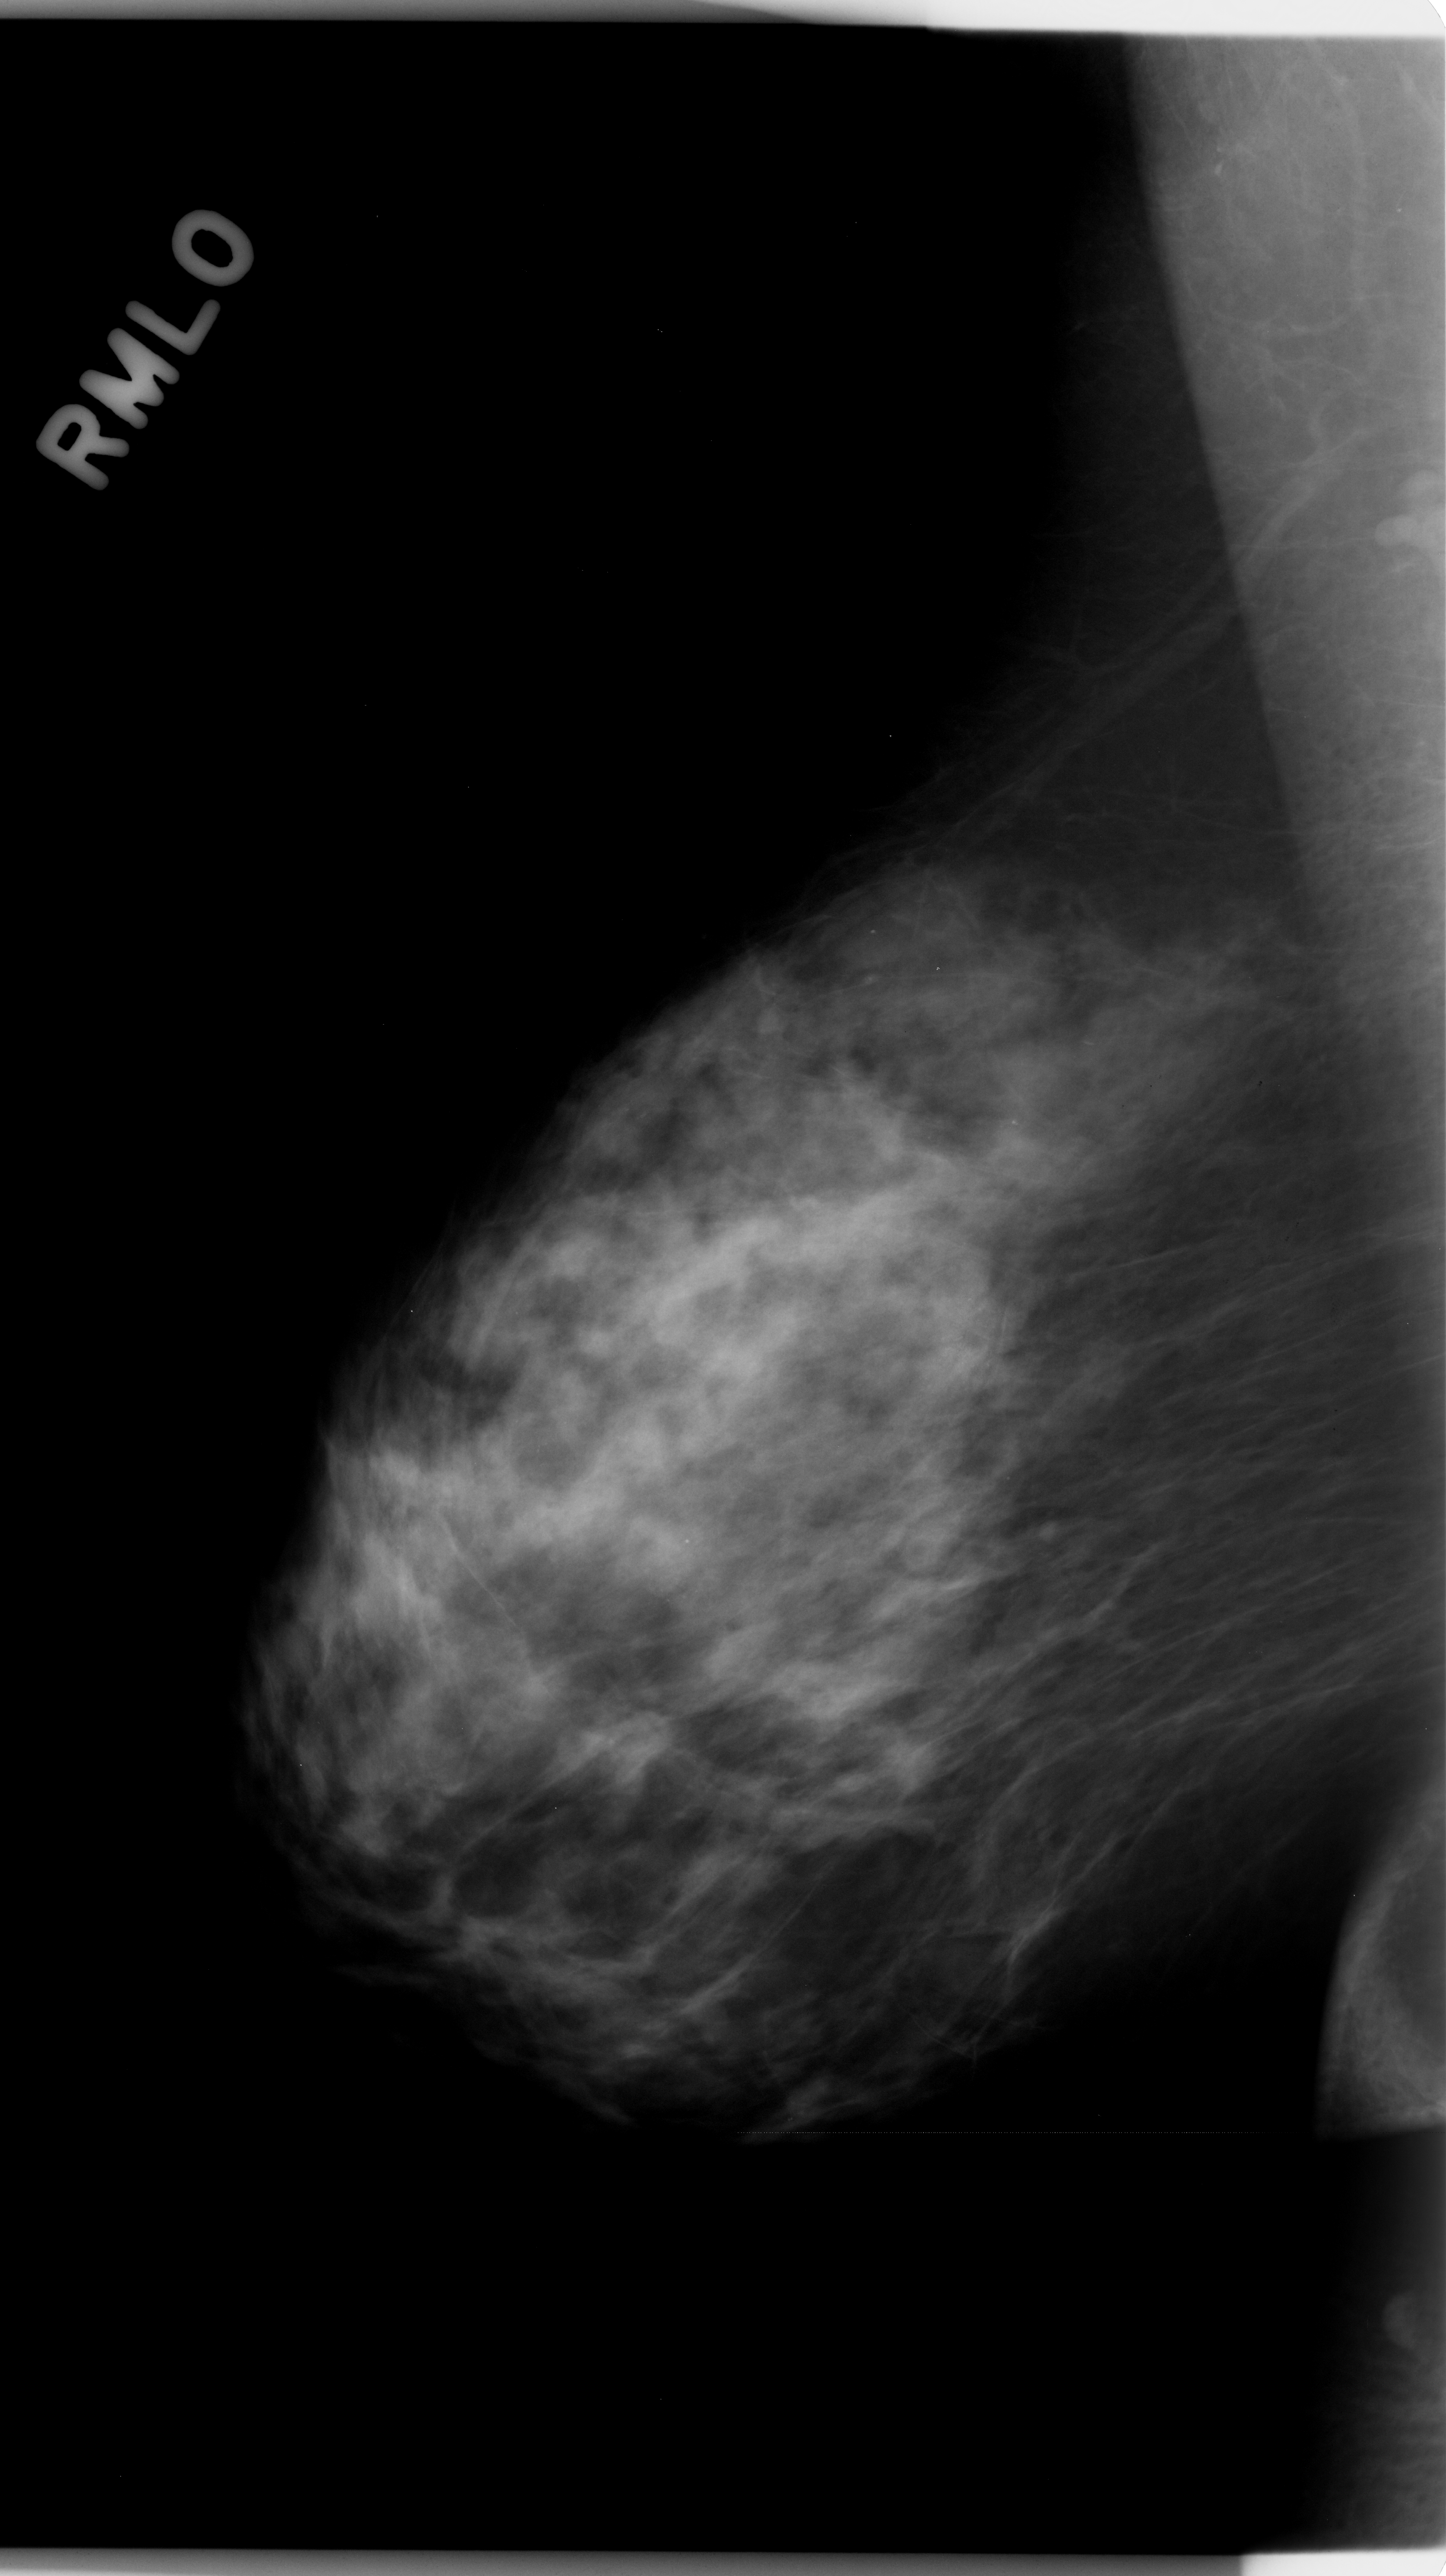
Scanned film-screen mammogram; right breast; mediolateral oblique (MLO) view; breast composition: heterogeneously dense (BI-RADS density category 3 of 4); 1446 × 2576 image matrix.
Expert-marked regions of interest on this film, with their recorded descriptors:
- calcifications, morphology amorphous, distribution clustered; BI-RADS assessment category 4; pathology (as recorded): benign: box from (x=866, y=1214) to (x=1057, y=1447) px